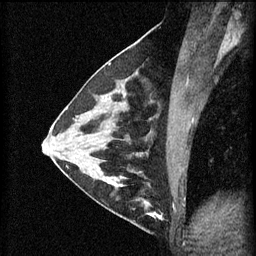
Breast MRI (dynamic contrast-enhanced), one sagittal slice. Position 29 of 60 along the scan axis. 3 images stored at this slice position (order not interpretable as contrast timing). 1.5 T. TE 4.2 ms, TR 11 ms. 2 mm slice thickness. 256 × 256 image matrix. Female patient, age 29 years.
Annotated regions visible in this slice (semi-automatically segmented with operator editing):
- analysis volume of interest (the breast-tissue region the enhancement analysis was run in; not a lesion): bounding box <105,172,171,227> (left, top, right, bottom; pixels)
- tumour enhancement mask (voxels above the 70 % enhancement threshold inside the analysis volume of interest): <105,172,165,221>